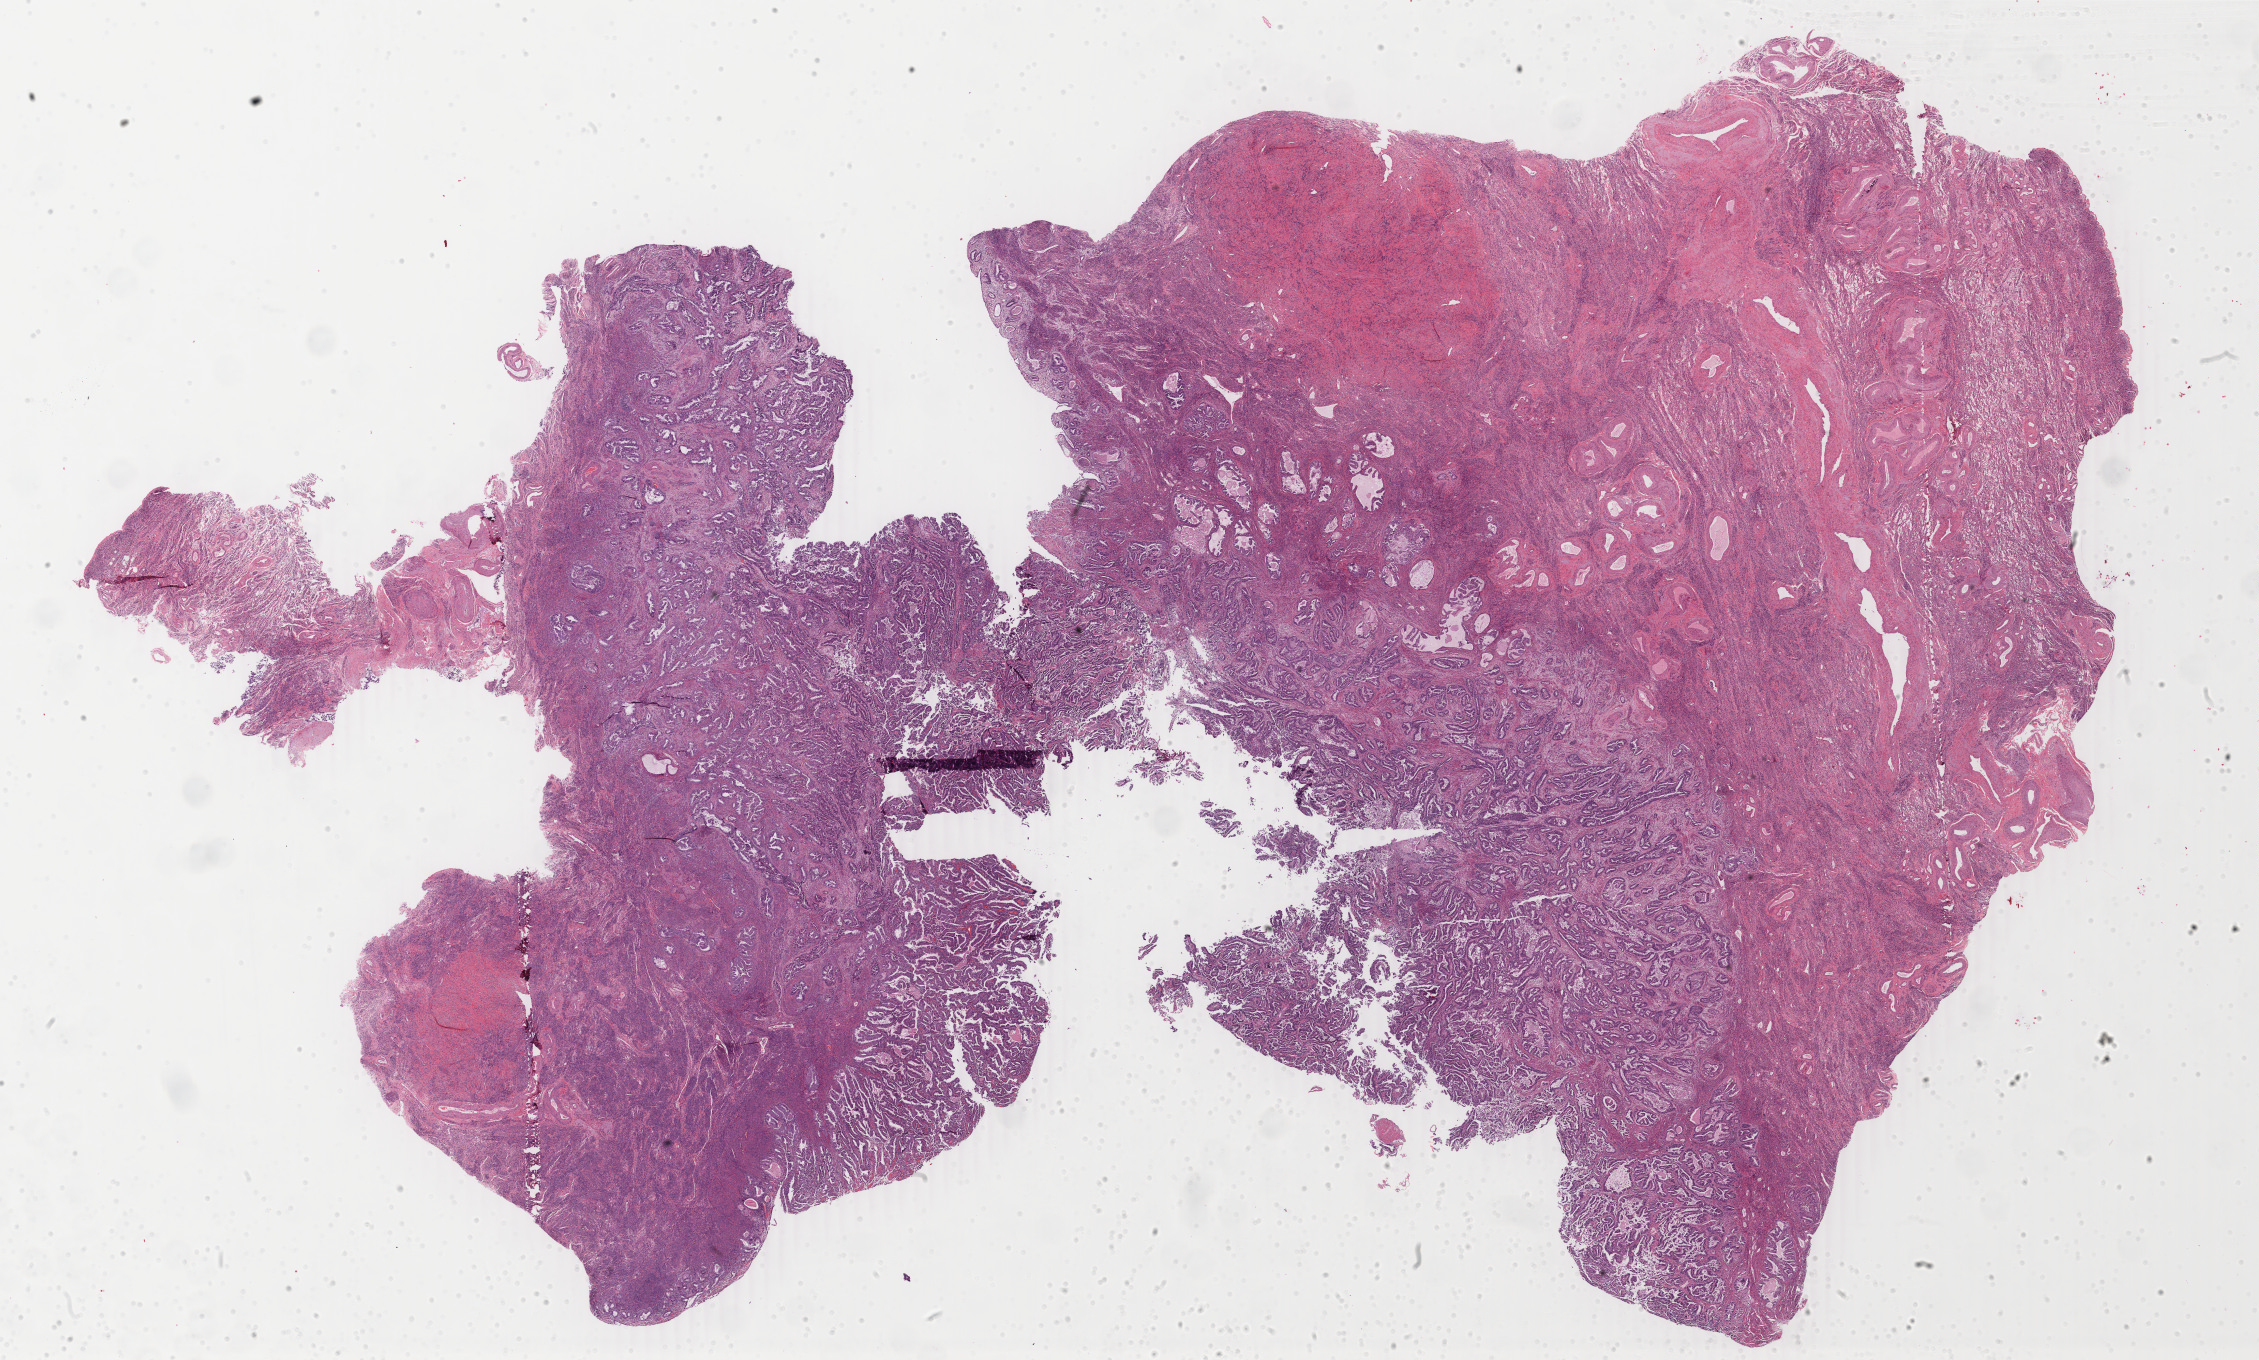
Whole-slide histology image, H&E-stained — a low-resolution overview of the entire scanned area, about 35.9 x 21.6 mm (acquisition: 40x scan), formalin-fixed paraffin-embedded (FFPE) diagnostic section, sample: primary tumour, uterus. Patient sex: female. Histologic grade: G2 (moderately differentiated).
* FIGO stage: IB
* pathologic diagnosis: Endometrioid adenocarcinoma, NOS (endometrium)